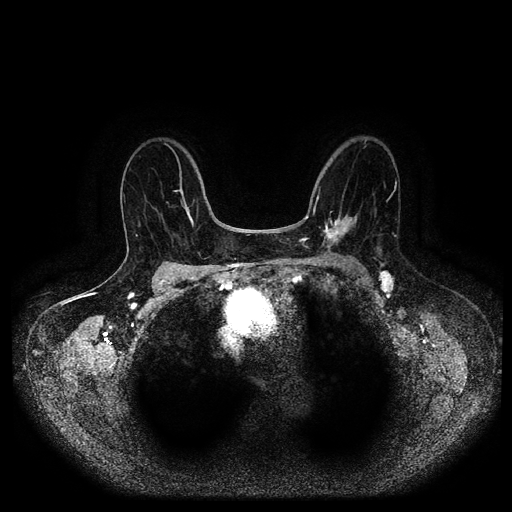
Breast MRI (dynamic contrast-enhanced, multi-phase), one axial slice. Position 60 of 116 along the scan axis. Dynamic contrast-enhanced series, time point 2 of 5 at this slice position (early post-contrast). 1.5 T. TE 2.6 ms, TR 5.2 ms. 2 mm slice thickness. 512 × 512 image matrix, field of view 380 × 380 mm. Patient: female, 69 years.
Annotated regions visible in this slice (semi-automatic segmentation, software-assisted and operator-edited):
- breast lesion (labelled 'tumour' in the annotation; benign lesions carry a separate 'benign' label): bounding box <319,205,360,253> (left, top, right, bottom; pixels)